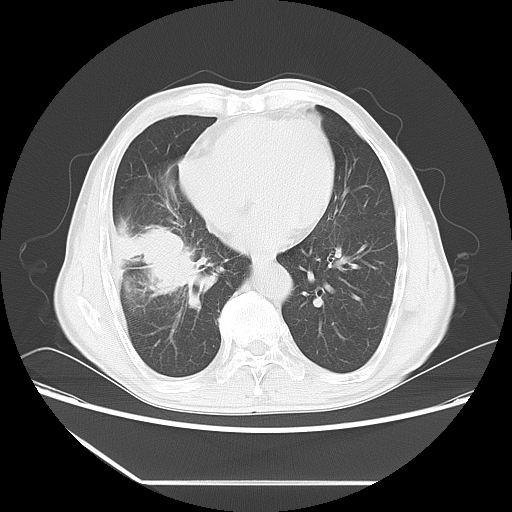
Chest CT, one axial slice. Slice 24 of 60 in the series (ordered by position). Reconstruction kernel LUNG. 120 kVp. Lung window (W 1500 / L -600 HU). 512 × 512 image matrix, field of view 386 × 386 mm. Male patient, age 72 years. Case-level facts recorded for this patient, not image findings: clinical TNM (as recorded): T1c N0 M0.
Structures marked on this image (bounding box drawn by a radiologist):
- lung tumour (recorded histology: squamous cell carcinoma): bounding box [x1, y1, x2, y2] px = [119, 212, 200, 298]